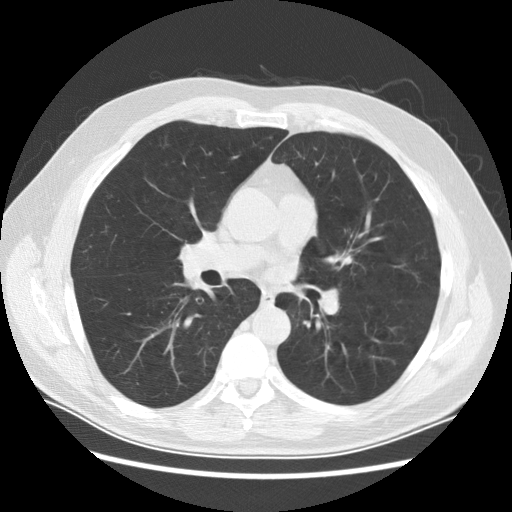
Axial slice from a low-dose chest CT screening exam. Baseline screening round. Lung window (W 1500 / L -600 HU). 2.5 mm slice thickness. Standard (soft-tissue) reconstruction kernel (STANDARD). 512 × 512 image matrix, field of view 370 × 370 mm. Male participant, aged 61 years at enrolment. Former smoker at enrolment.
Lesion marked by an expert reader, box from (x=224, y=274) to (x=260, y=311) px. Screening reader's record for this exam: no non-calcified nodule ≥4 mm recorded. Official screen result: negative screen, minor abnormalities not suspicious for lung cancer. Lung cancer was diagnosed 756 days after this screen (after the third annual screen): squamous cell carcinoma, keratinizing, NOS, right lower lobe, stage IIIB (AJCC 6th edition), 40 mm at pathology.